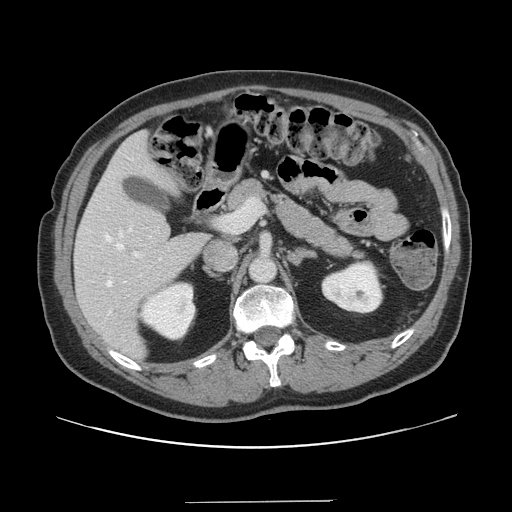
Contrast-enhanced abdominal CT, one axial slice. Position 81 of 151 along the scan axis. Intravenous contrast given. Soft-tissue window (W 400 / L 40 HU). 2.5 mm slice thickness. 512 × 512 image matrix, field of view 399 × 399 mm. Male patient, age 63 years. Case-level facts recorded for this patient, not image findings: diagnosis: colorectal cancer liver metastases, imaged before liver resection; multiple liver metastases: no; largest metastasis: 2.1 cm; disease in both lobes: no.
Outlined on this slice (manually delineated by an expert):
- hepatic veins: bounding box (x1, y1, x2, y2) in pixels: (105, 232, 124, 287)
- liver: (75, 133, 209, 359)
- planned liver remnant (the part of the liver to remain after resection): (76, 132, 208, 359)
- portal vein (with intrahepatic branches): (133, 198, 260, 258)